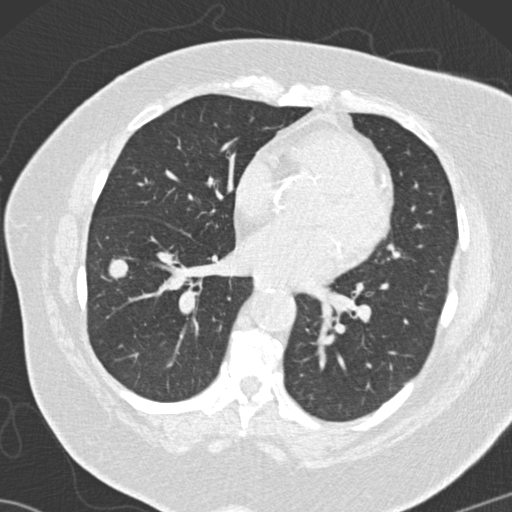
Low-dose screening chest CT, one axial slice; slice 61 of 146 in the series (ordered by position); lung window (W 1500 / L -600 HU); 2 mm slice thickness; 512 × 512 image matrix.
Annotated regions visible in this slice (expert manual segmentation):
- lesion 2 (tumor, lower lobe of right lung): box from (x=107, y=258) to (x=130, y=281) px